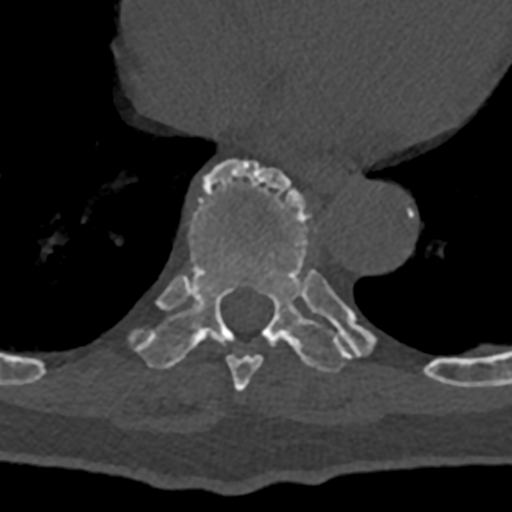
CT including the spine, one axial slice; position 674 of 797 along the scan axis; reconstruction kernel Br40s/3; bone window (W 1800 / L 400 HU); 0.5 mm slice thickness; 512 × 512 image matrix. Patient: male, 74 years. Case-level facts recorded for this patient, not image findings: primary cancer: renal; vertebrae with lytic lesions (as recorded): T10, L1, L2, L3, L4, L5.
Structures marked on this image (semi-automatic segmentation, software-assisted and operator-edited):
- T8 vertebra: bounding box [x1, y1, x2, y2] px = [226, 355, 263, 391]
- T9 vertebra: [131, 160, 432, 377]